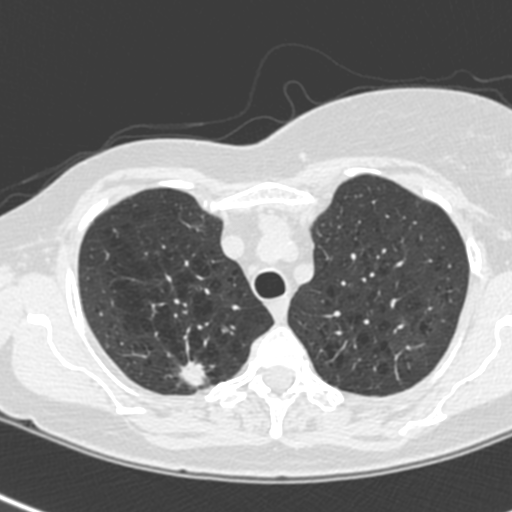
Low-dose screening chest CT, one axial slice; slice 178 of 214 in the series (ordered by position); lung window (W 1500 / L -600 HU); 1.3 mm slice thickness; 512 × 512 image matrix.
Annotated regions visible in this slice (expert manual segmentation):
- lesion 1 (tumor, upper lobe of right lung): box from (x=180, y=362) to (x=206, y=388) px